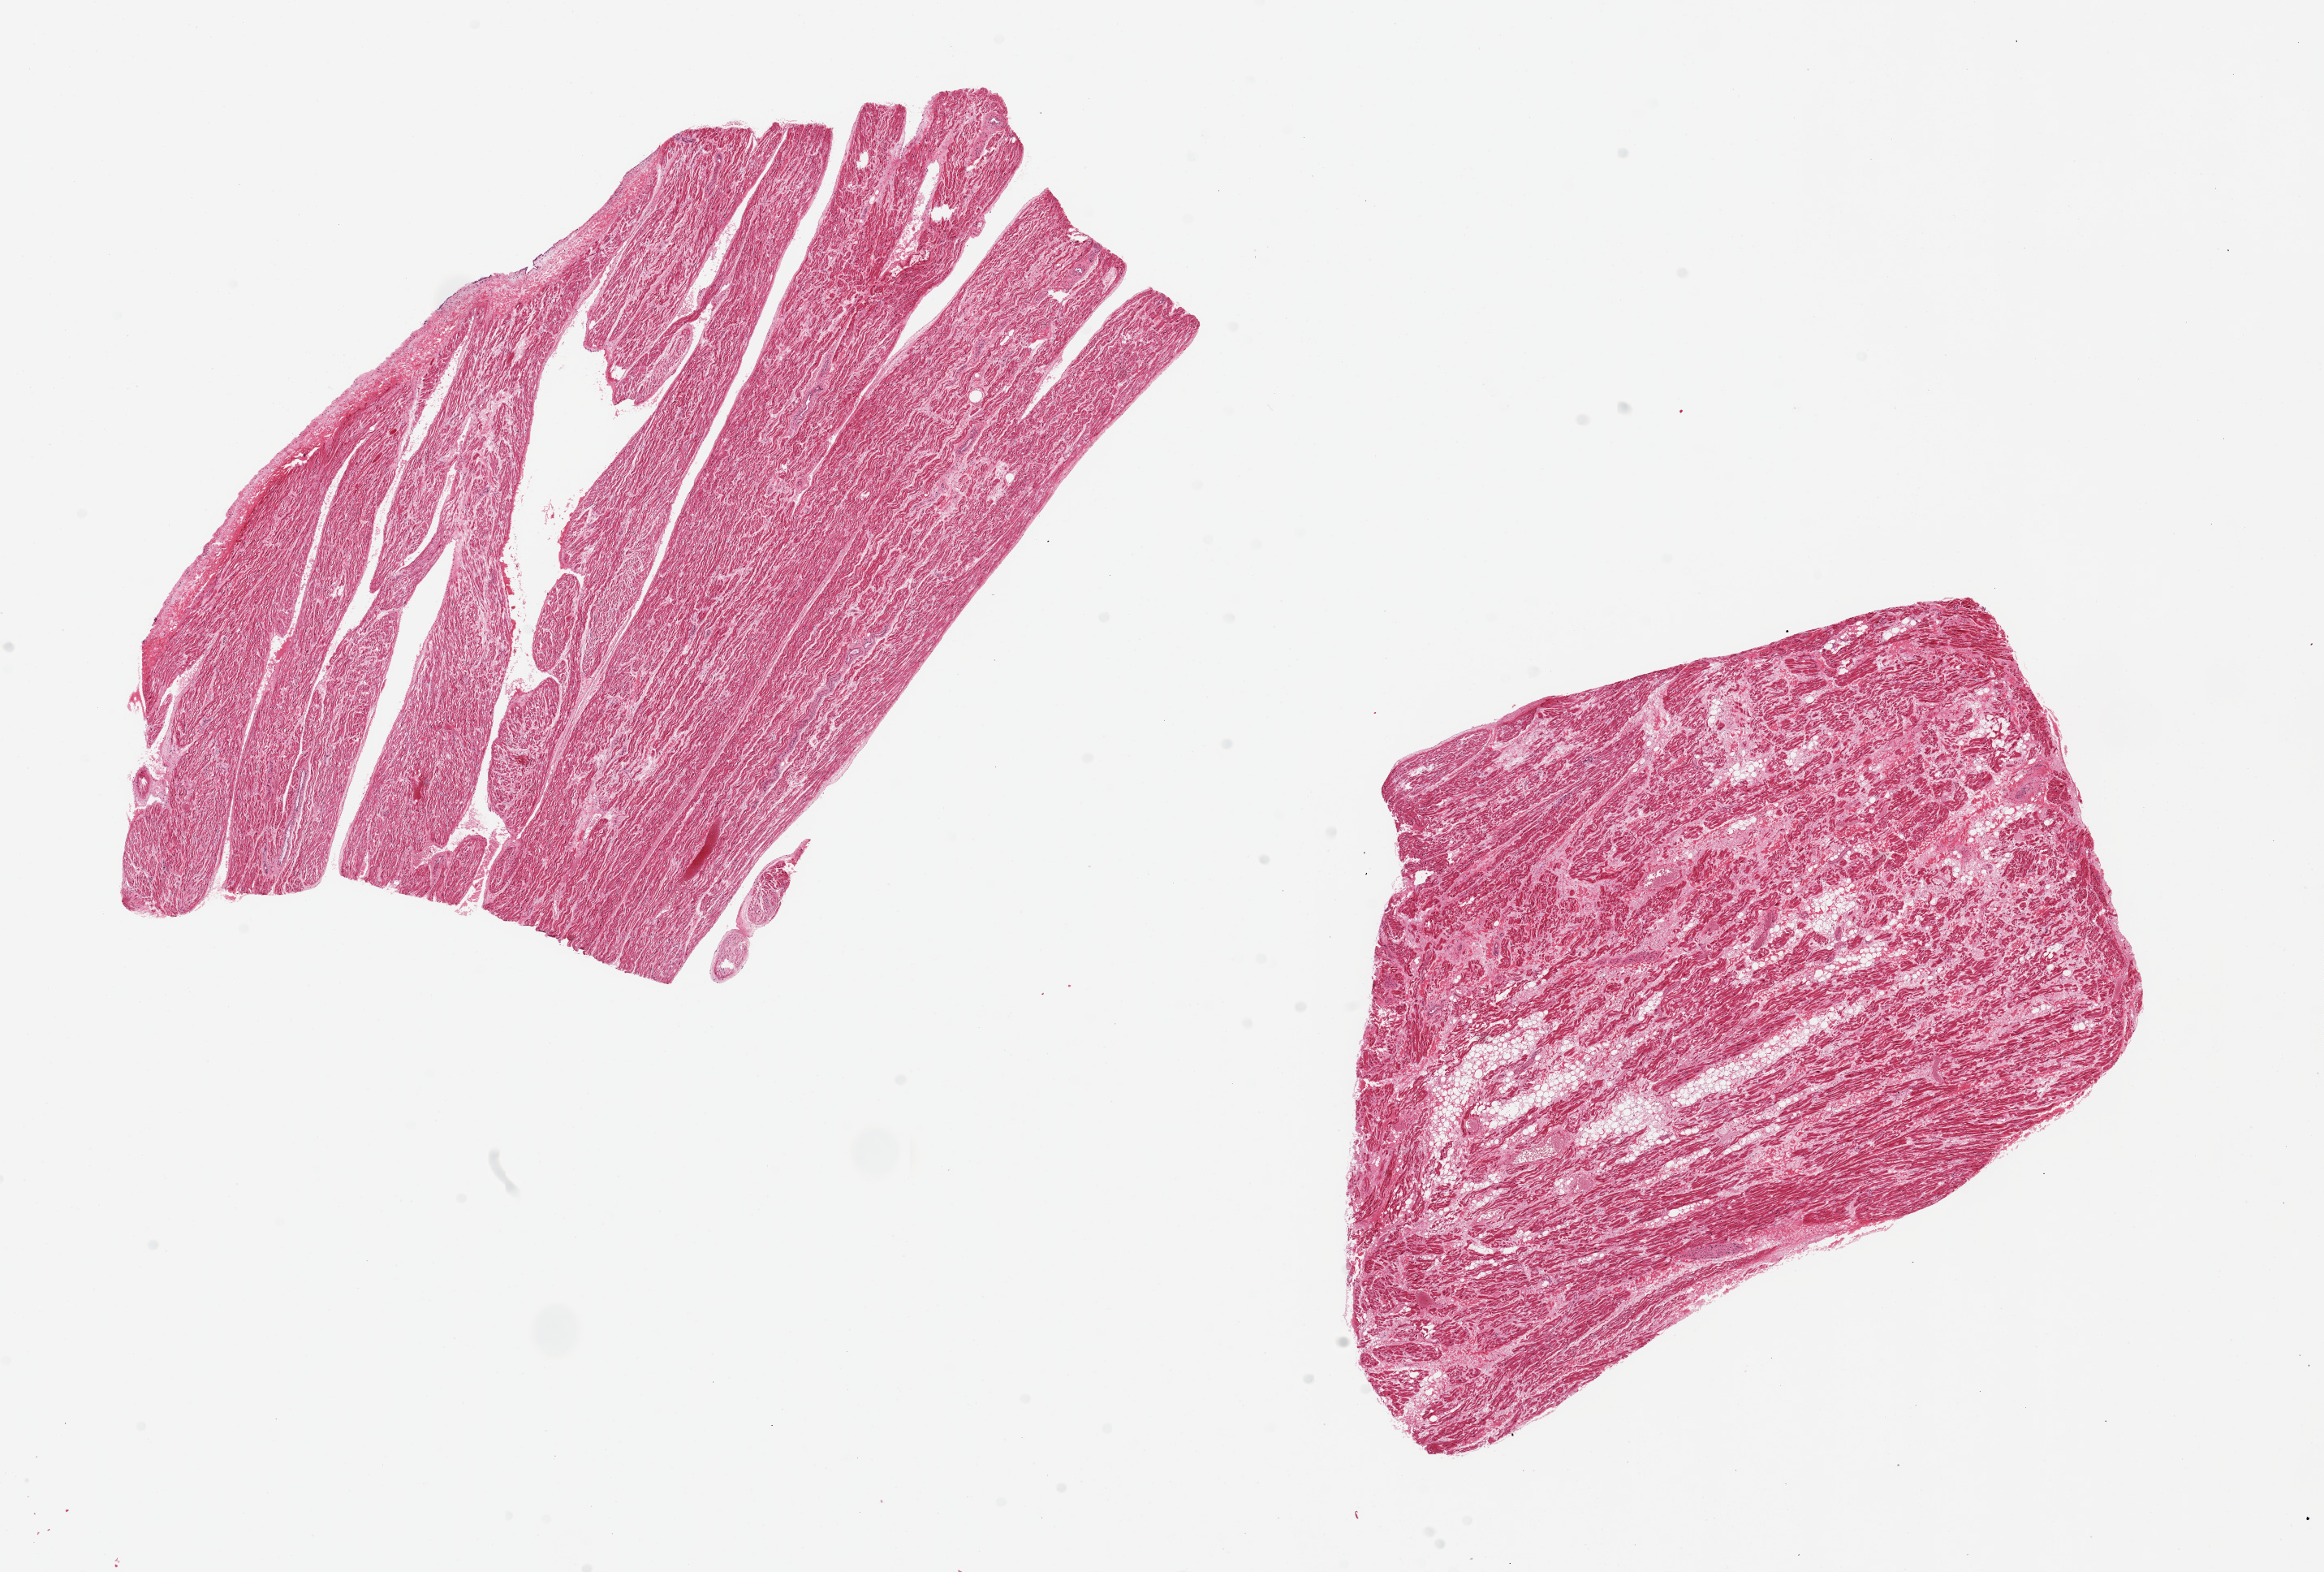
Whole-slide image, H&E stain, a low-resolution overview of the entire scanned area, about 22.6 x 15.3 mm (acquisition: 20x scan), PAXgene-fixed, paraffin-embedded tissue, section of auricular appendage (target tissue), tissue donor sample. Male donor.
Pathologist's review note for this sample: 2 pieces ~ ~9x6mm.